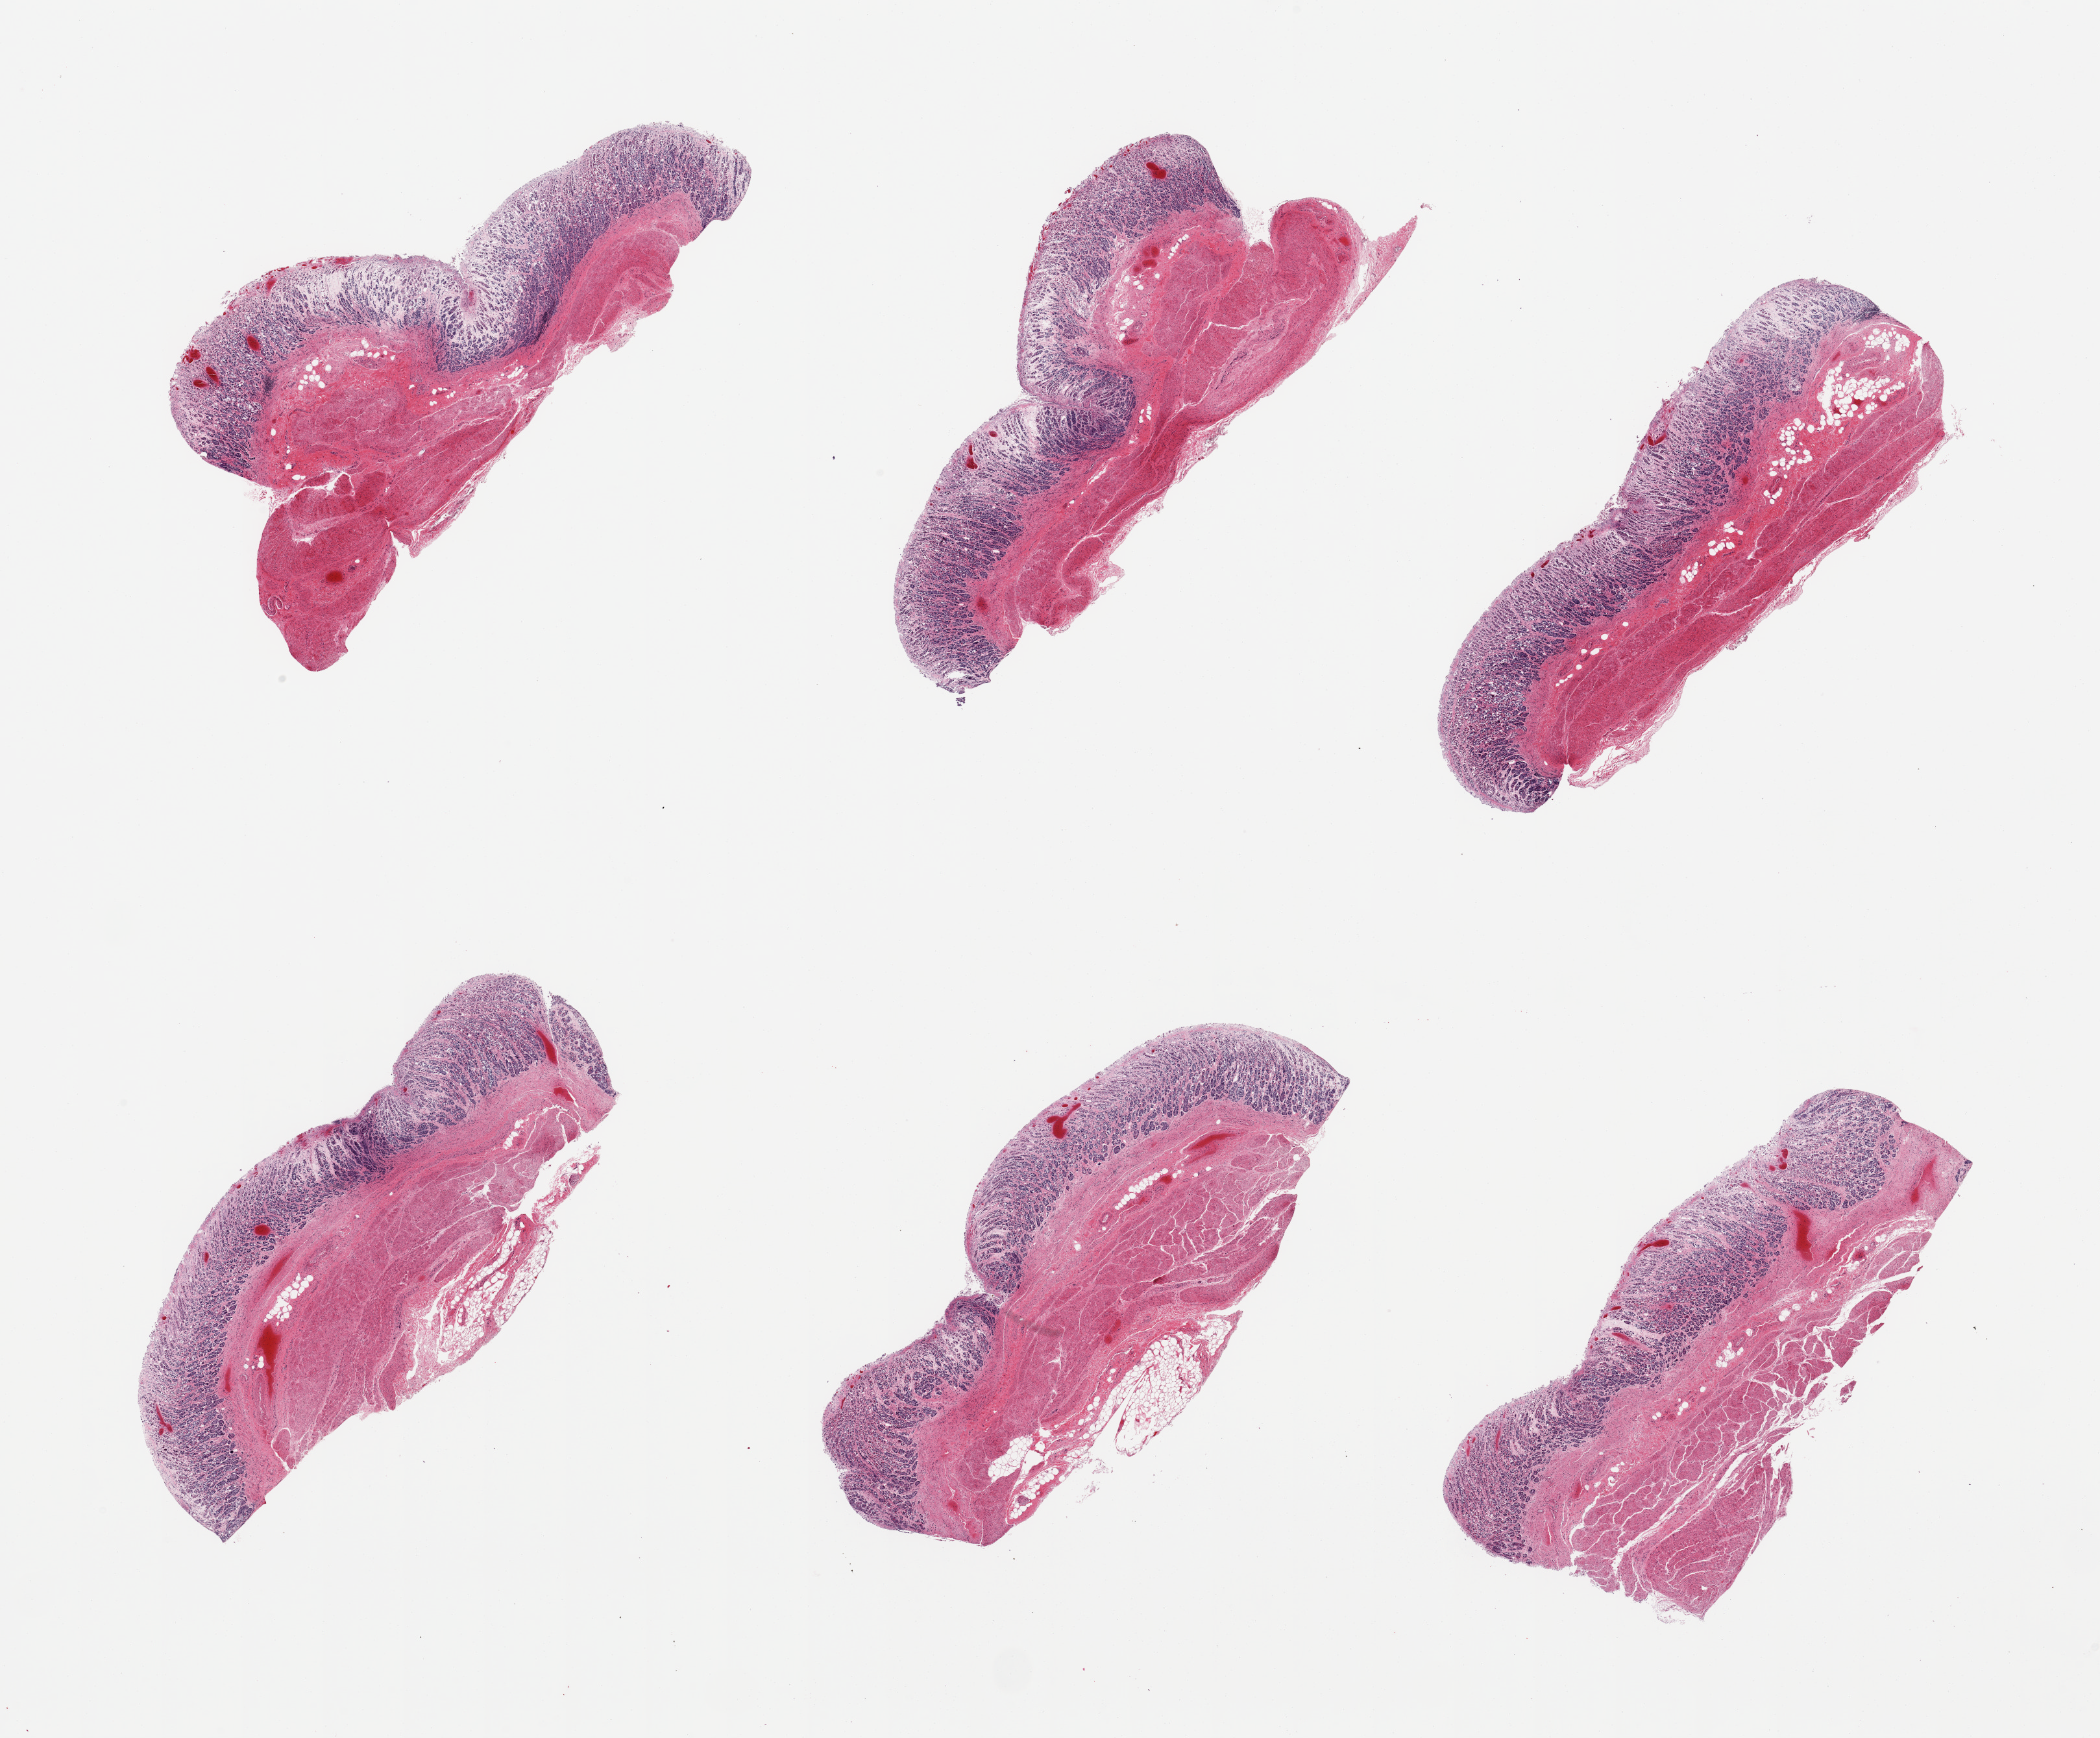
H&E whole-slide image, brightfield — a low-resolution overview of the entire scanned area, about 25.6 x 21.2 mm (slide scanned at 20x). PAXgene-fixed, paraffin-embedded tissue. Sampled site (target tissue): stomach. Donor tissue sample.
Reviewer comment on this tissue sample: 6 pieces, mucosa up to ~1mm, modeate adavance autolysis.